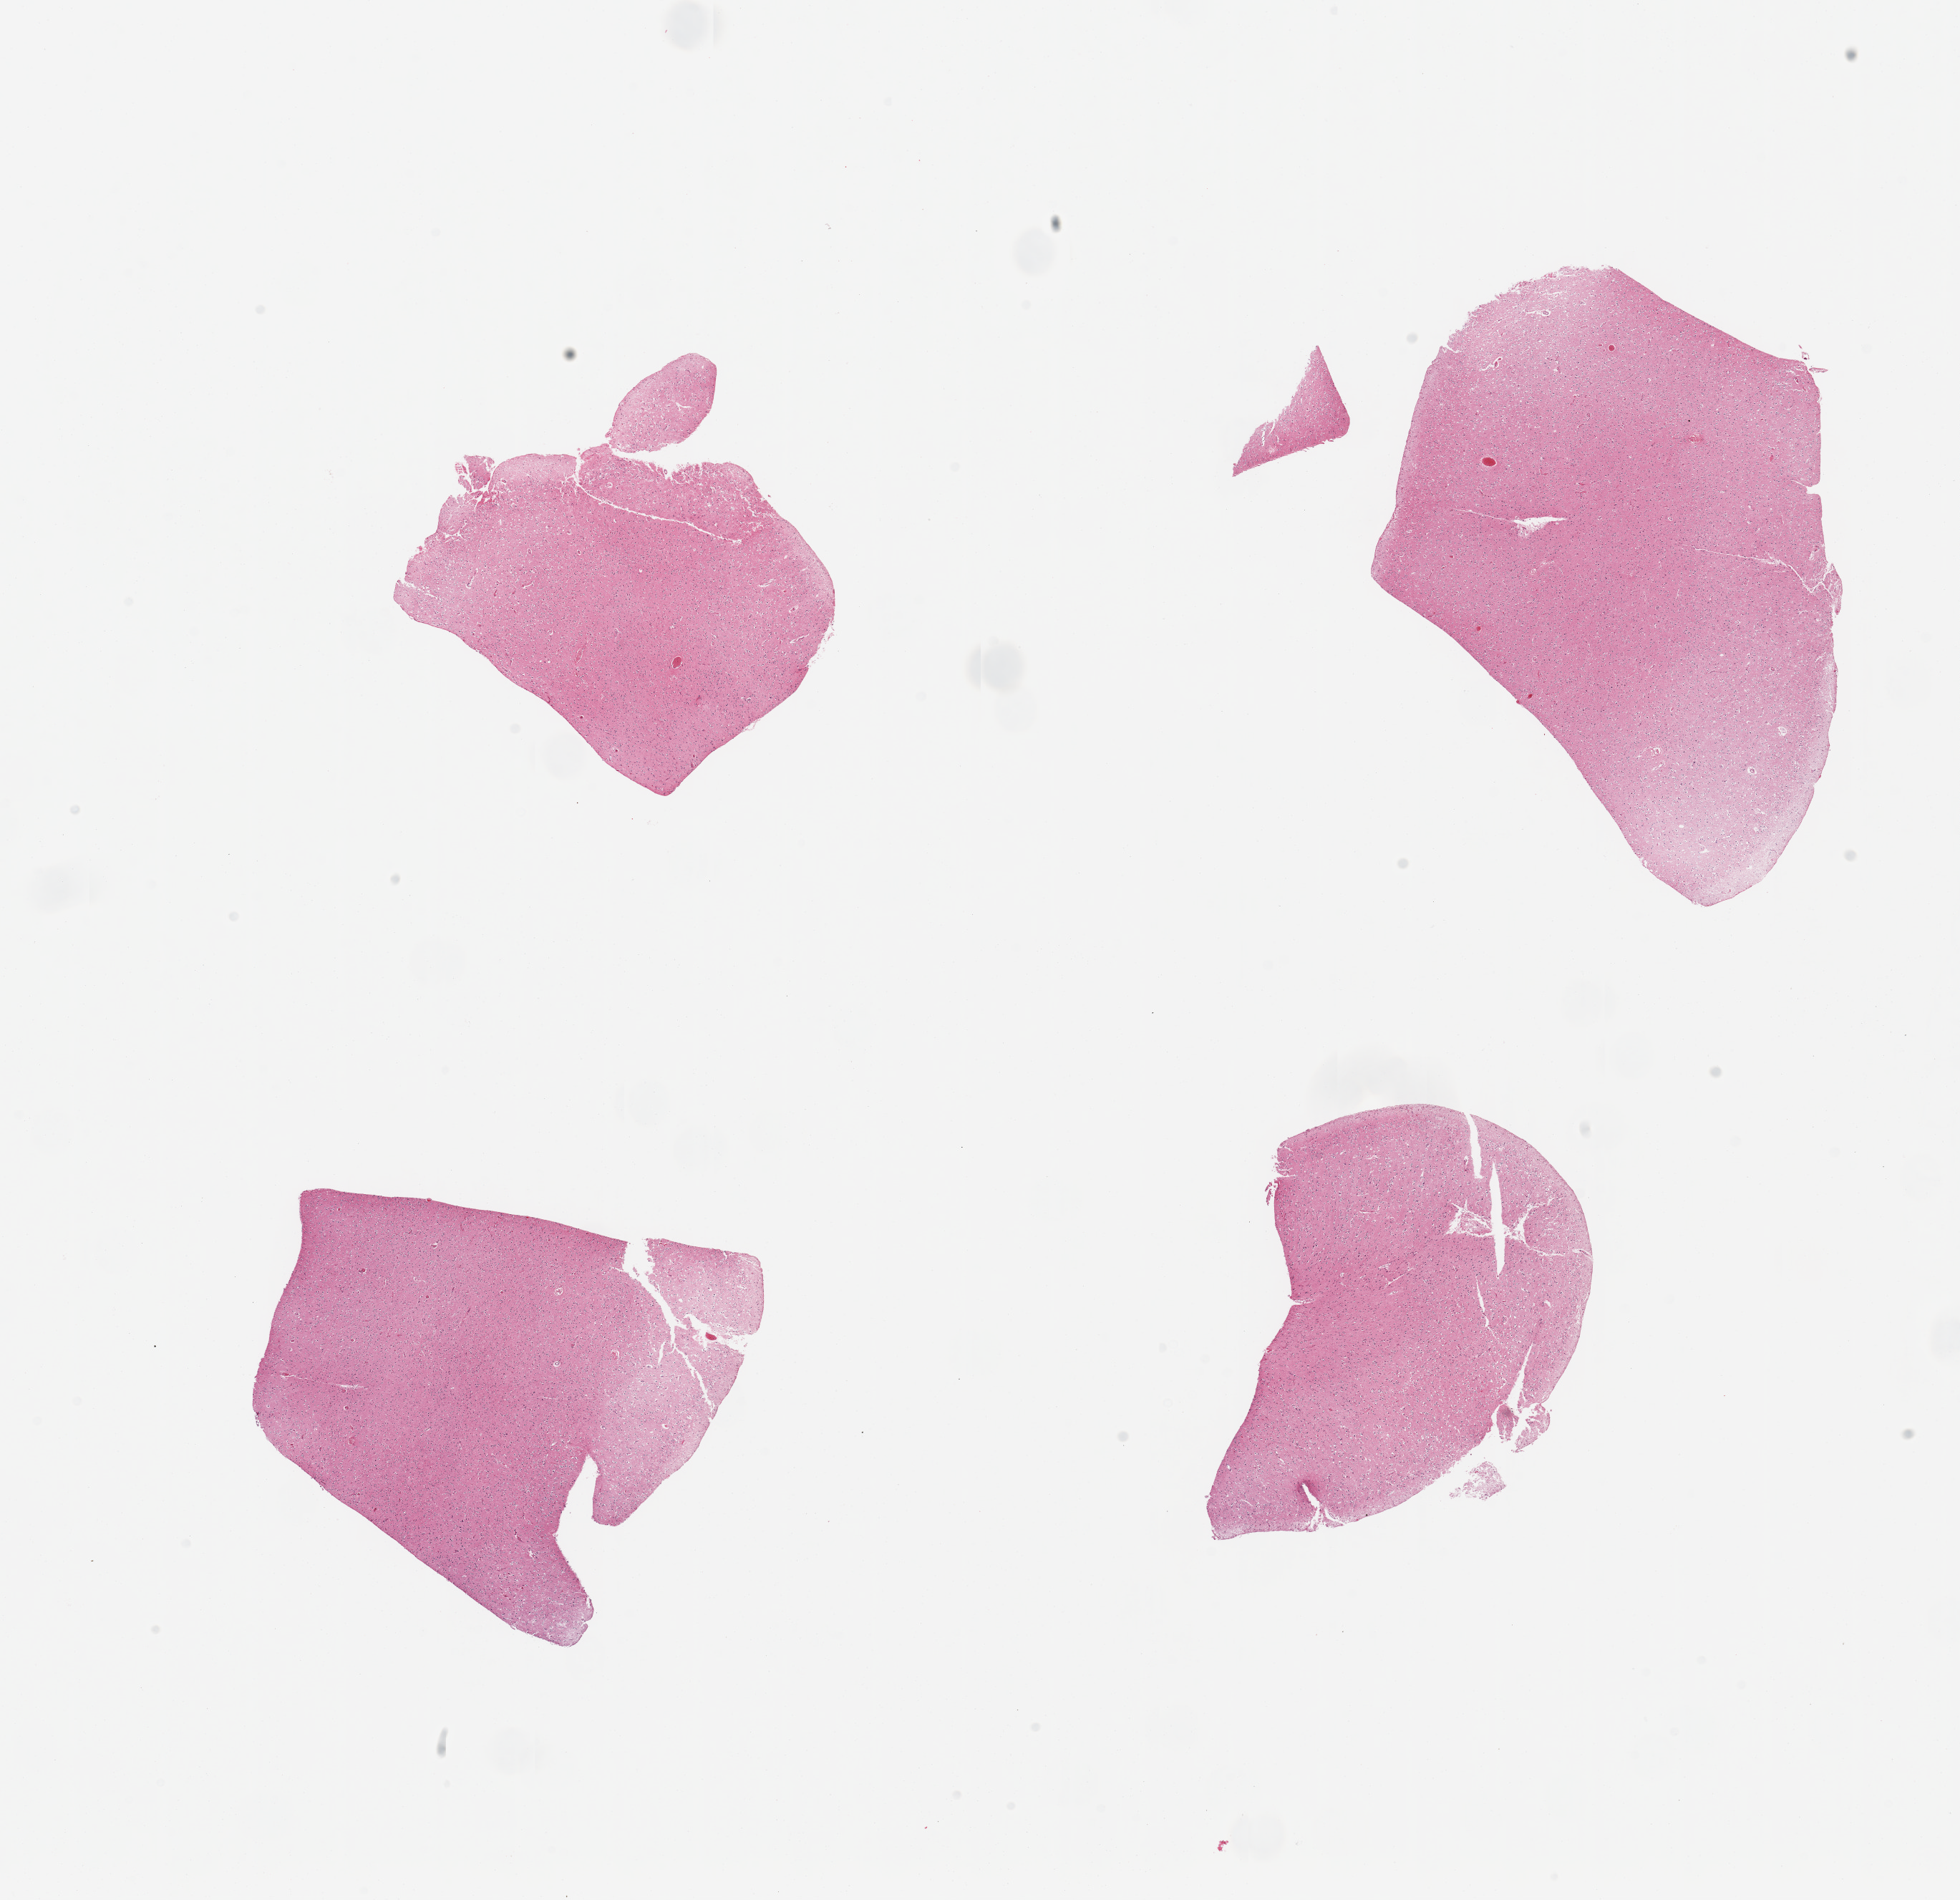
Hematoxylin and eosin (H&E) whole-slide image — a low-resolution overview of the entire scanned area, about 21.7 x 21.0 mm. PAXgene-fixed paraffin-embedded (PFPE) section. Target tissue: cerebral cortex. Tissue donor sample. Donor sex: male.
Reviewer comment on this tissue sample: 4 pieces.